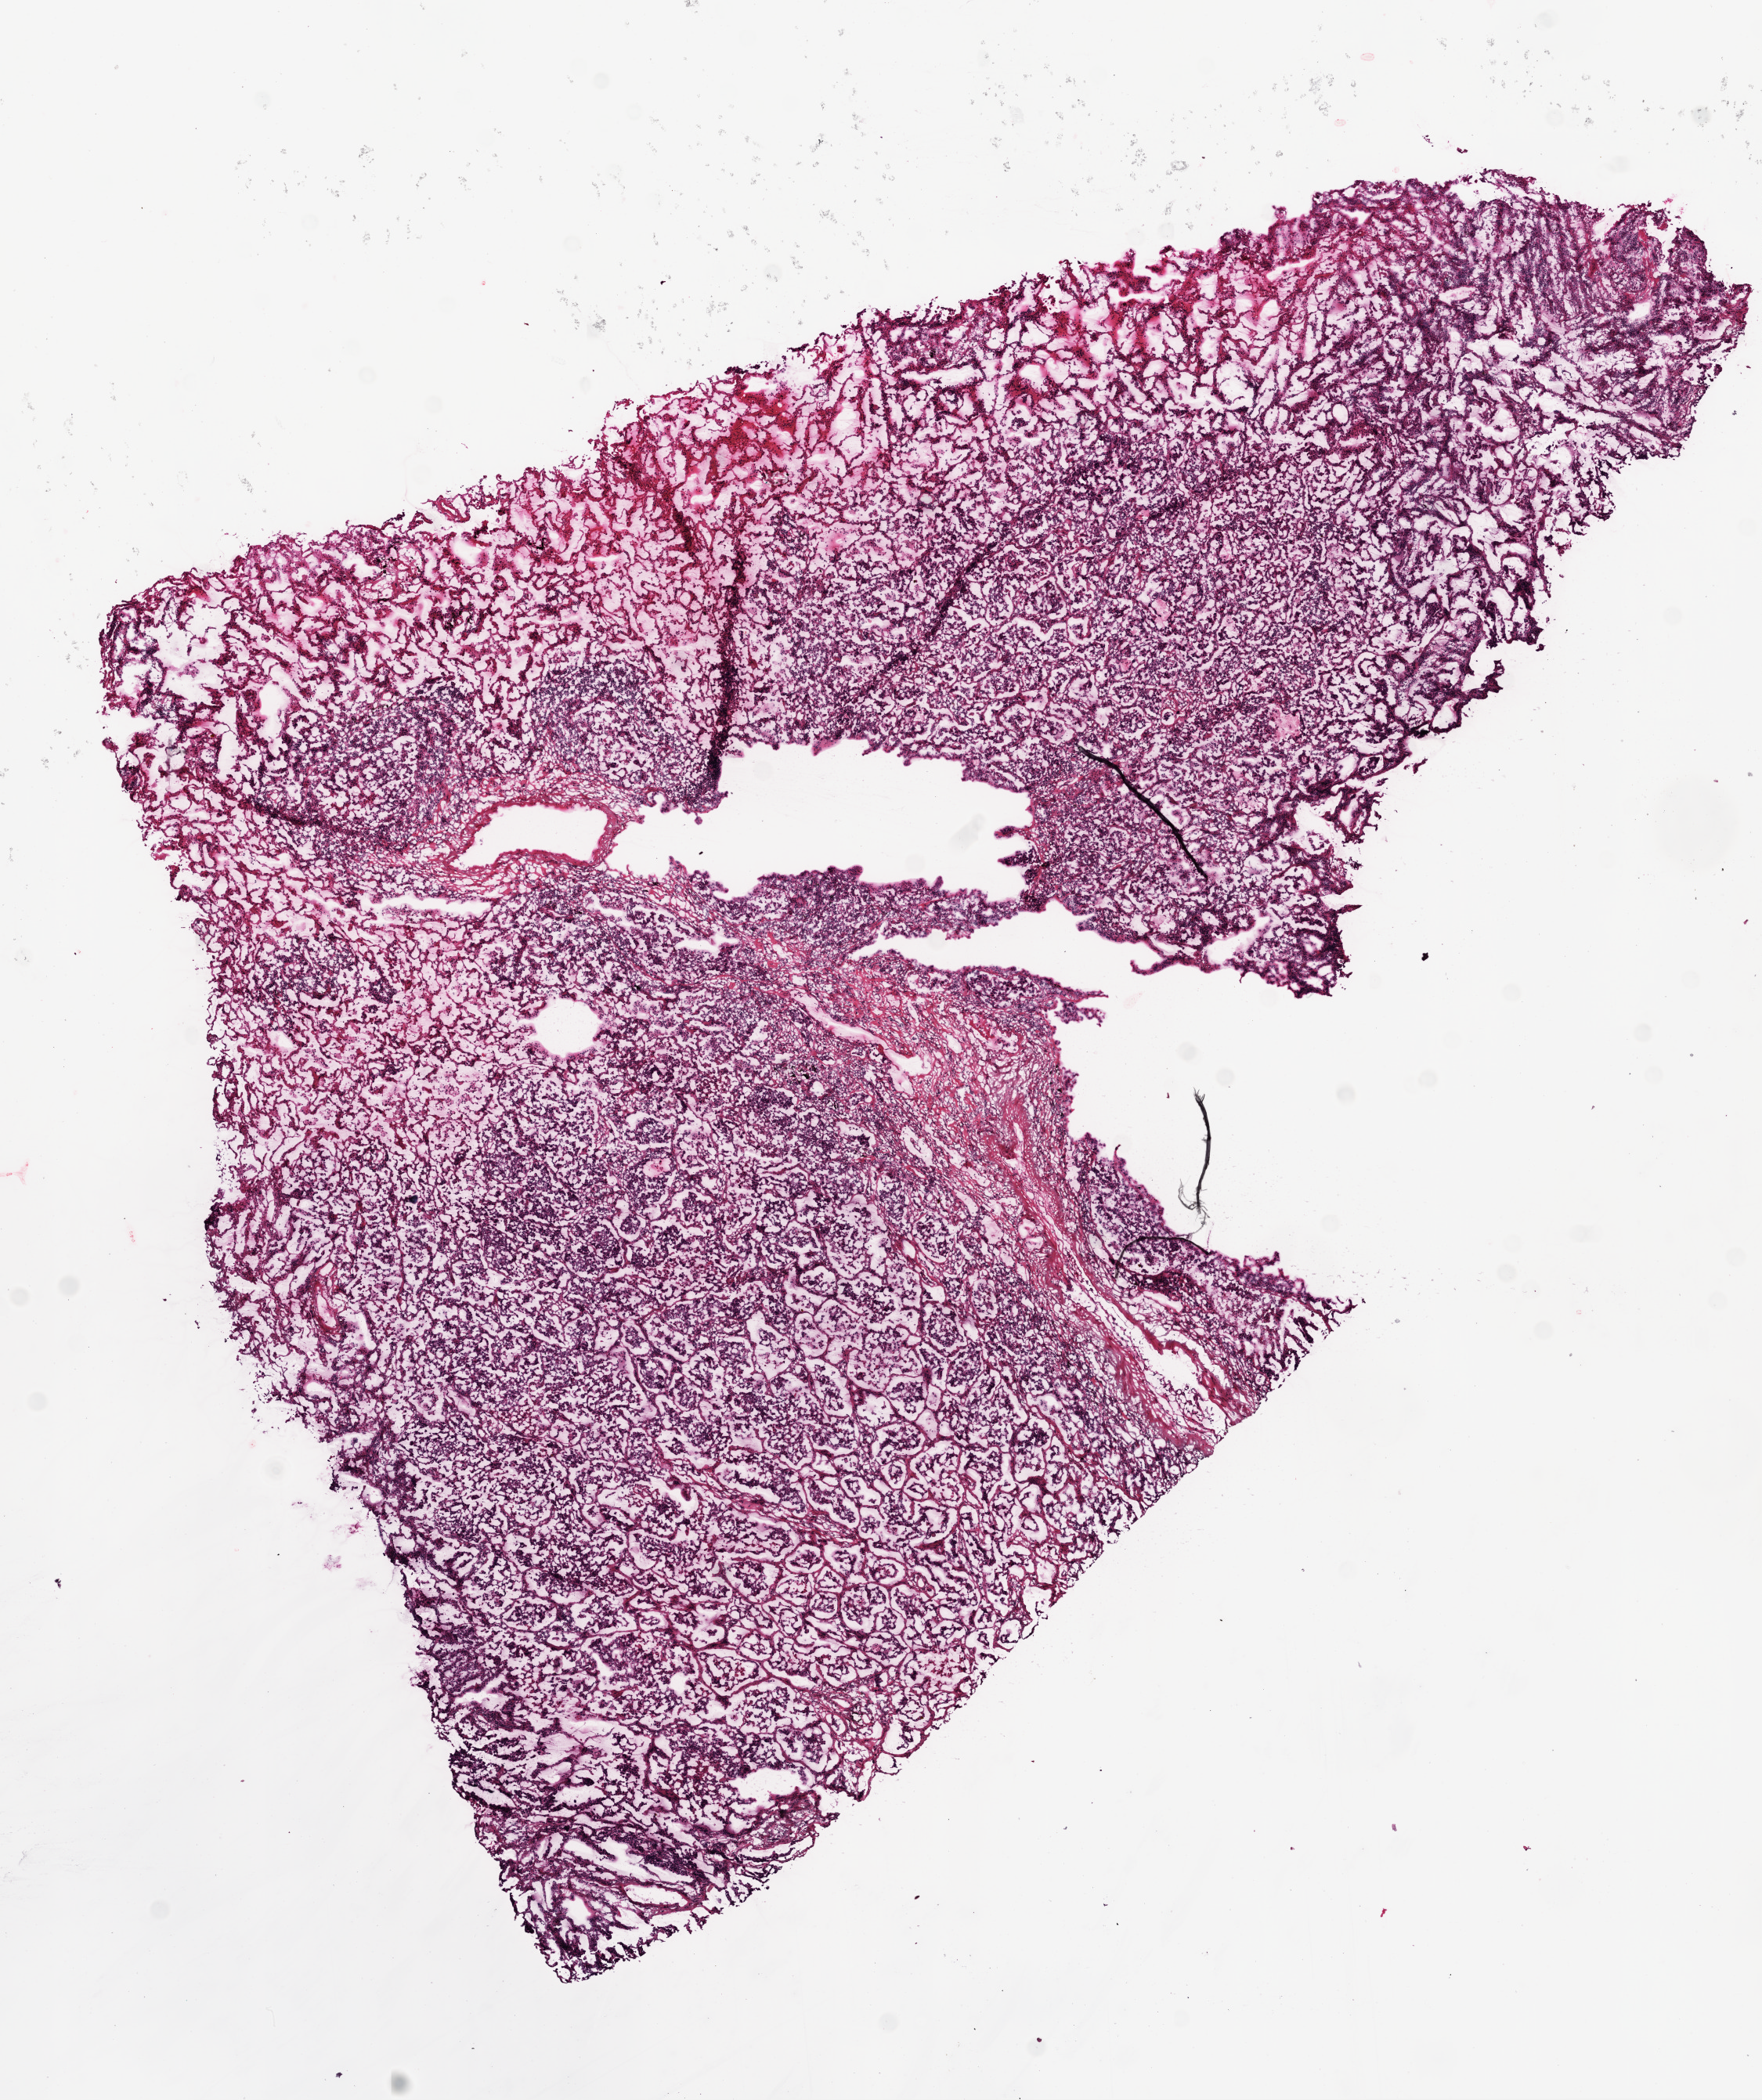
Whole-slide histology image, H&E — whole scanned area (about 9.0 x 10.8 mm, slide scanned at 20x) shown as a low-resolution overview. Frozen section. Lung, primary tumour sample. Female, age 77 years at initial diagnosis. Slide review estimates, as recorded: tumour cells 80%, tumour nuclei 90%, normal cells 5%, stromal cells 13%, necrosis 2%.
AJCC pathologic stage: IIIA. Pathologic diagnosis: Adenocarcinoma, NOS (upper lobe, lung). TNM: T2 N2 M0.